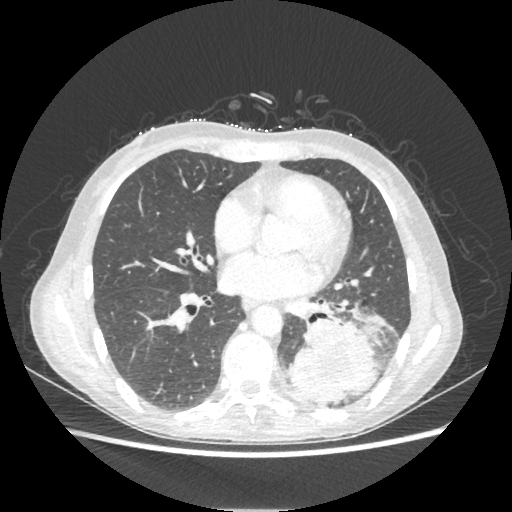
Chest CT, one axial slice; position 101 of 221 along the scan axis; 80 kVp; lung window (W 1500 / L -600 HU); 1.25 mm slice thickness; 512 × 512 image matrix, field of view 360 × 360 mm. Patient: female, 53 years. Case-level facts recorded for this patient, not image findings: clinical TNM (as recorded): T3 N0 M0.
Structures marked on this image (rectangle marked by the reading radiologist):
- lung tumour (recorded histology: adenocarcinoma): bounding box <285,320,379,404> (left, top, right, bottom; pixels)